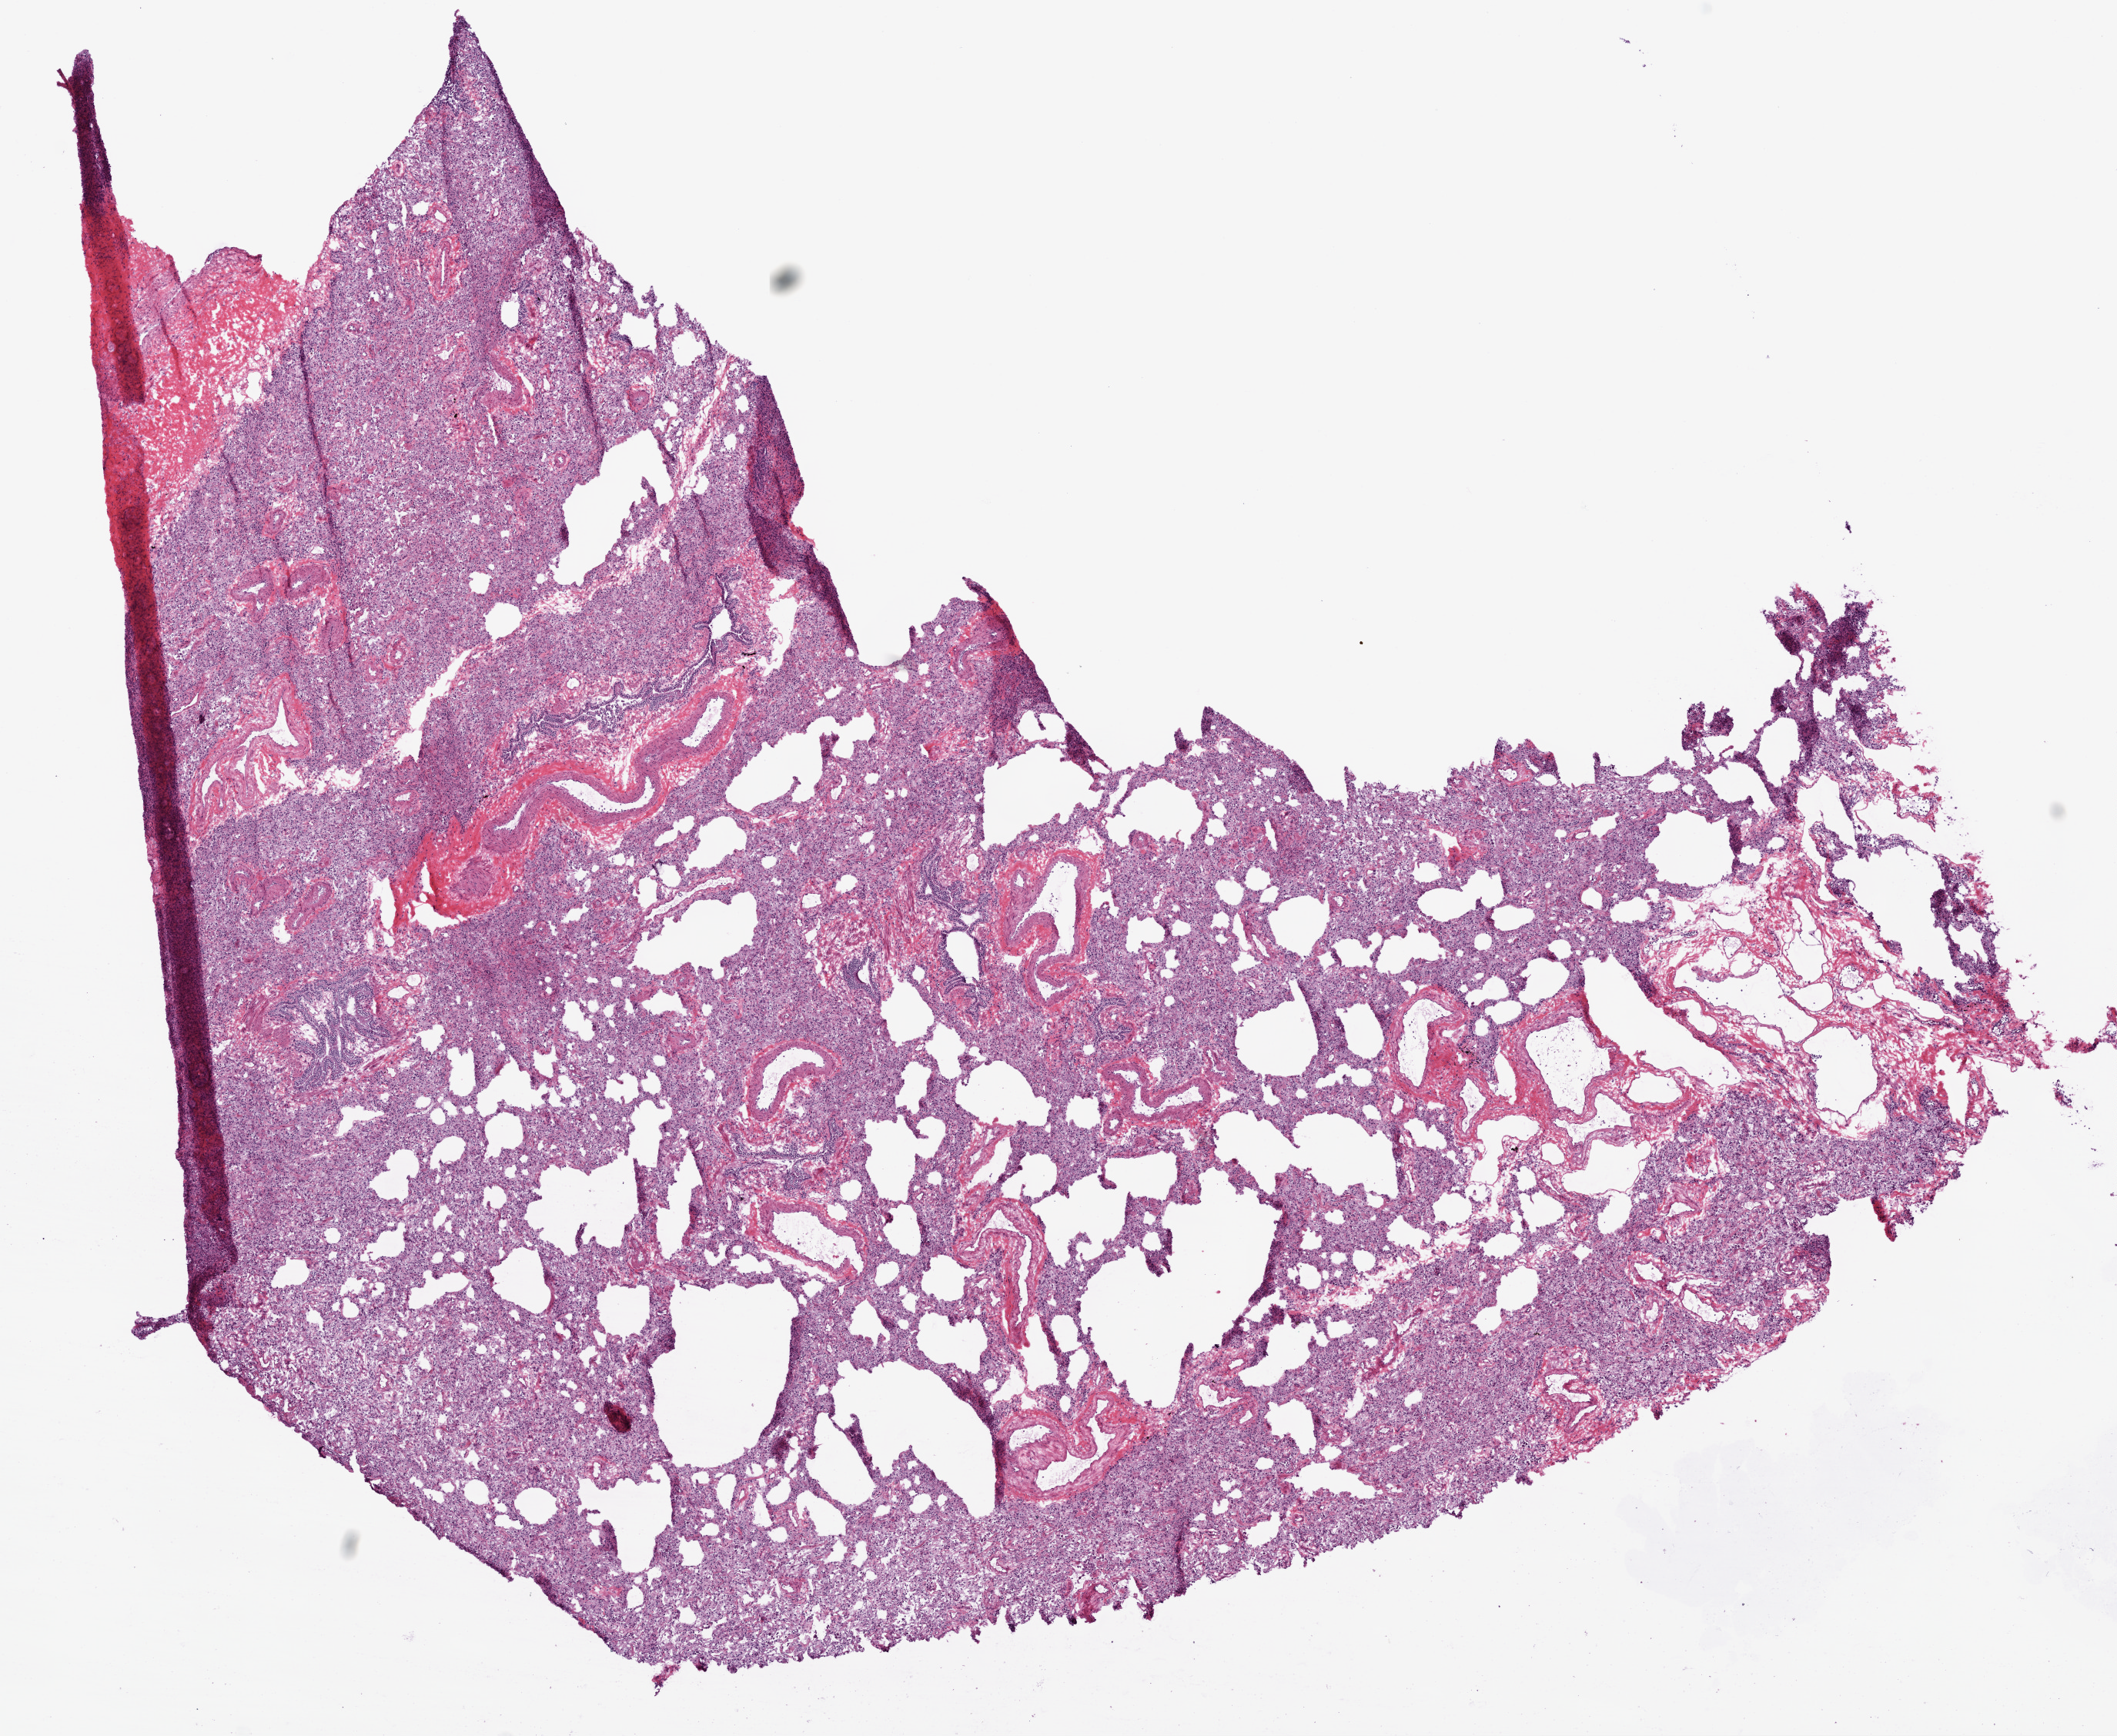
Digitized Hematoxylin and eosin (H&E) stained tissue section (whole slide) — a low-resolution overview of the entire scanned area, about 11.0 x 9.0 mm (acquisition: 20x scan), frozen section from the bottom of the tissue portion, lung, solid tissue normal (non-tumour tissue) sample. Male patient; age at initial diagnosis 66 years.
This section: solid tissue normal (non-tumour) sample from the same patient. Patient diagnosis: Squamous cell carcinoma, NOS (lower lobe, lung).